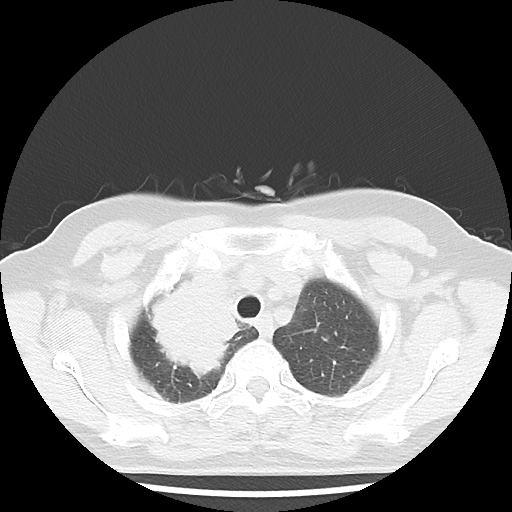
Chest CT, one axial slice. Slice 36 of 43 in the series (ordered by position). Reconstruction kernel LUNG. 100 kVp. Lung window (W 1500 / L -600 HU). 5 mm slice thickness. 512 × 512 image matrix, field of view 316 × 316 mm. Patient: female, 62 years. Case-level facts recorded for this patient, not image findings: clinical TNM (as recorded): T3 N0 M0.
Structures marked on this image (rectangle marked by the reading radiologist):
- lung tumour (recorded histology: small cell carcinoma): bounding box (x1, y1, x2, y2) in pixels: (134, 262, 254, 387)